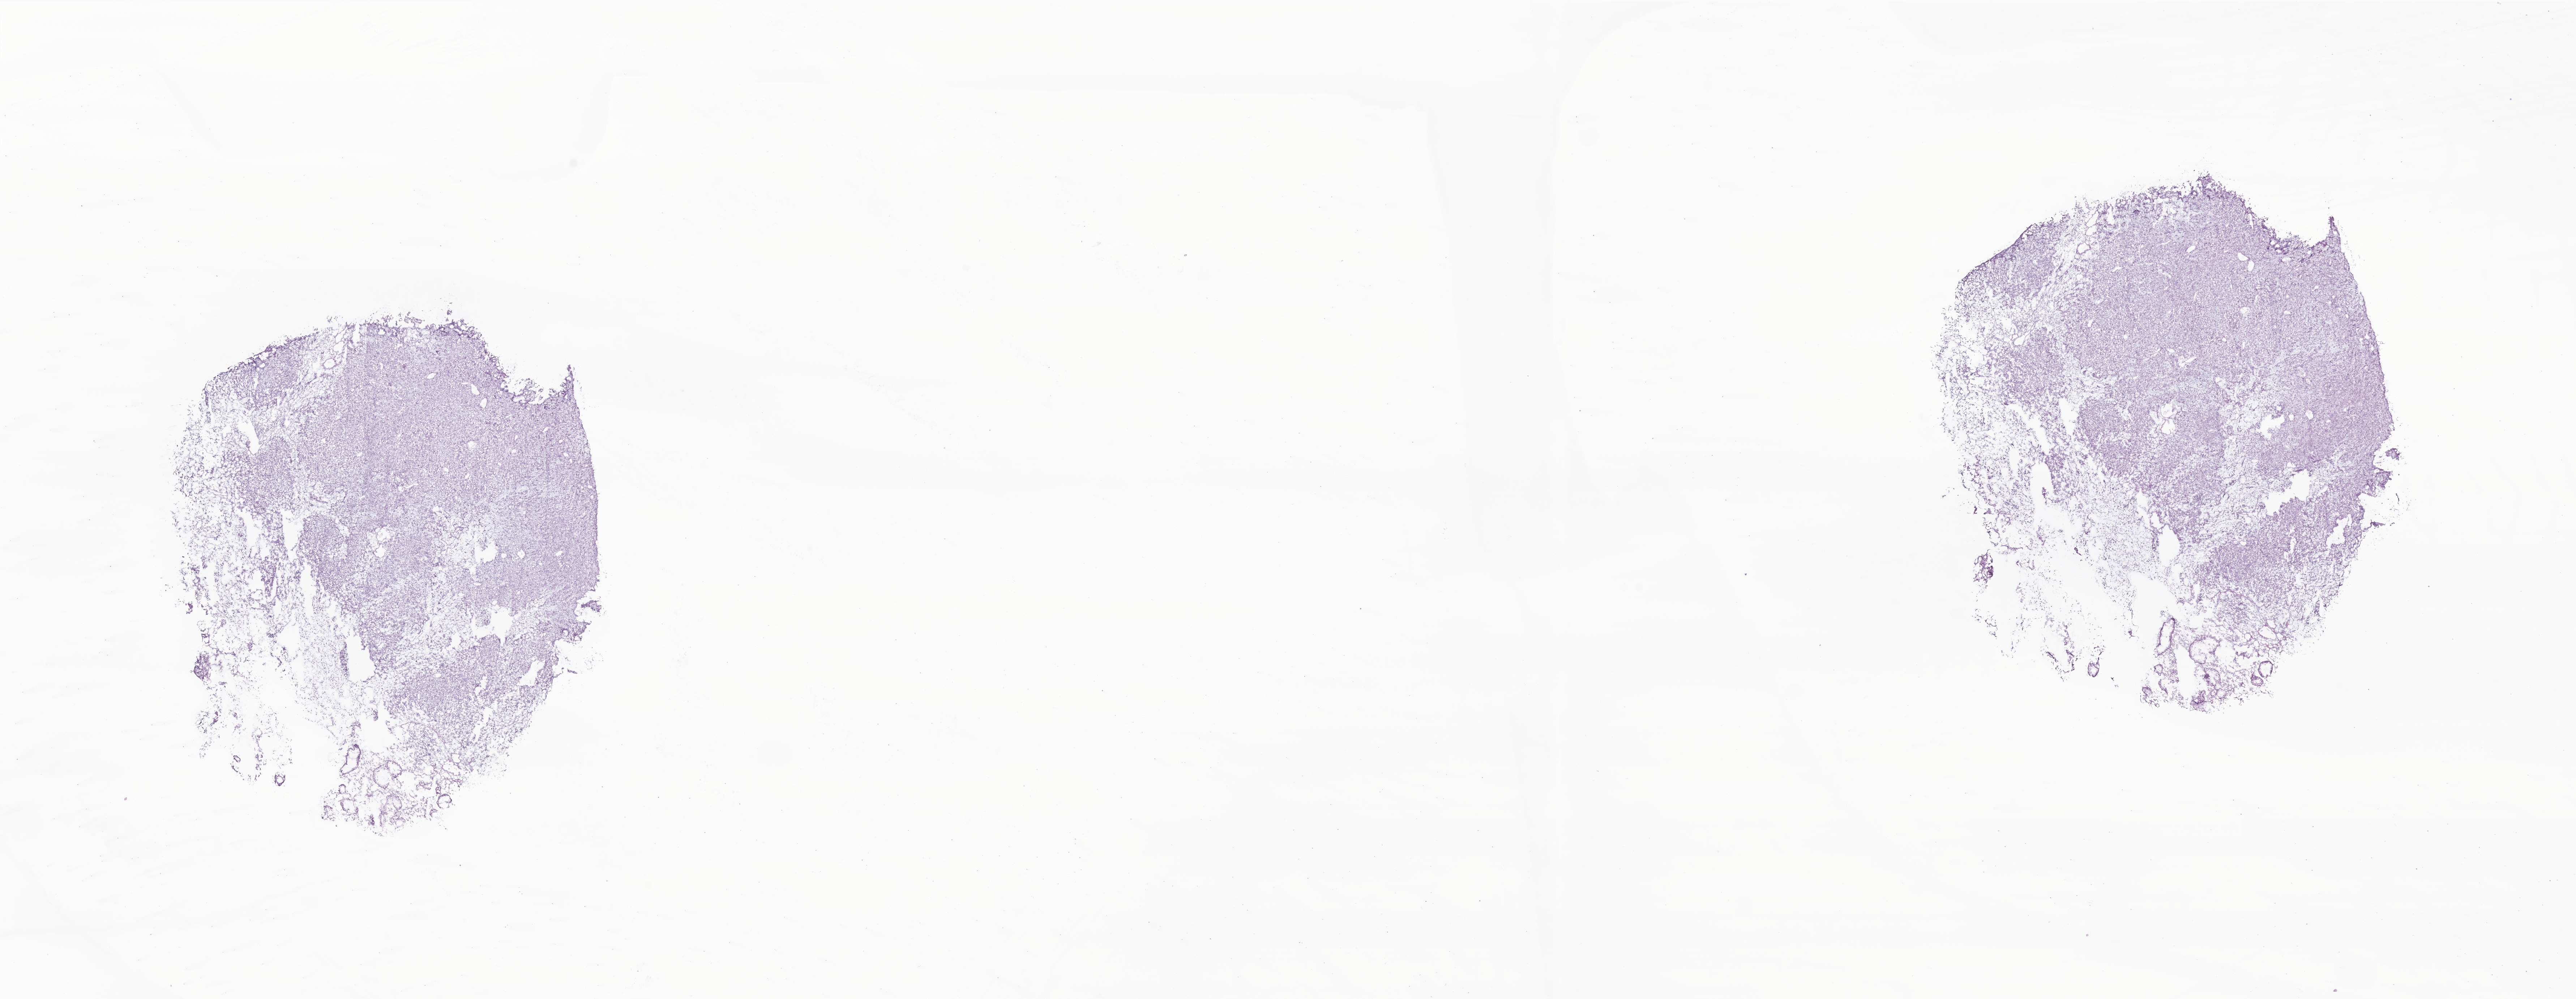
Digitized haematoxylin and eosin-stained section of tumor tissue from the stomach, whole scanned area (about 30.0 x 11.6 mm) shown as a low-resolution overview. Patient male; age 206 months (17 years 2 months).
Specimen: frozen section (OCT-embedded).